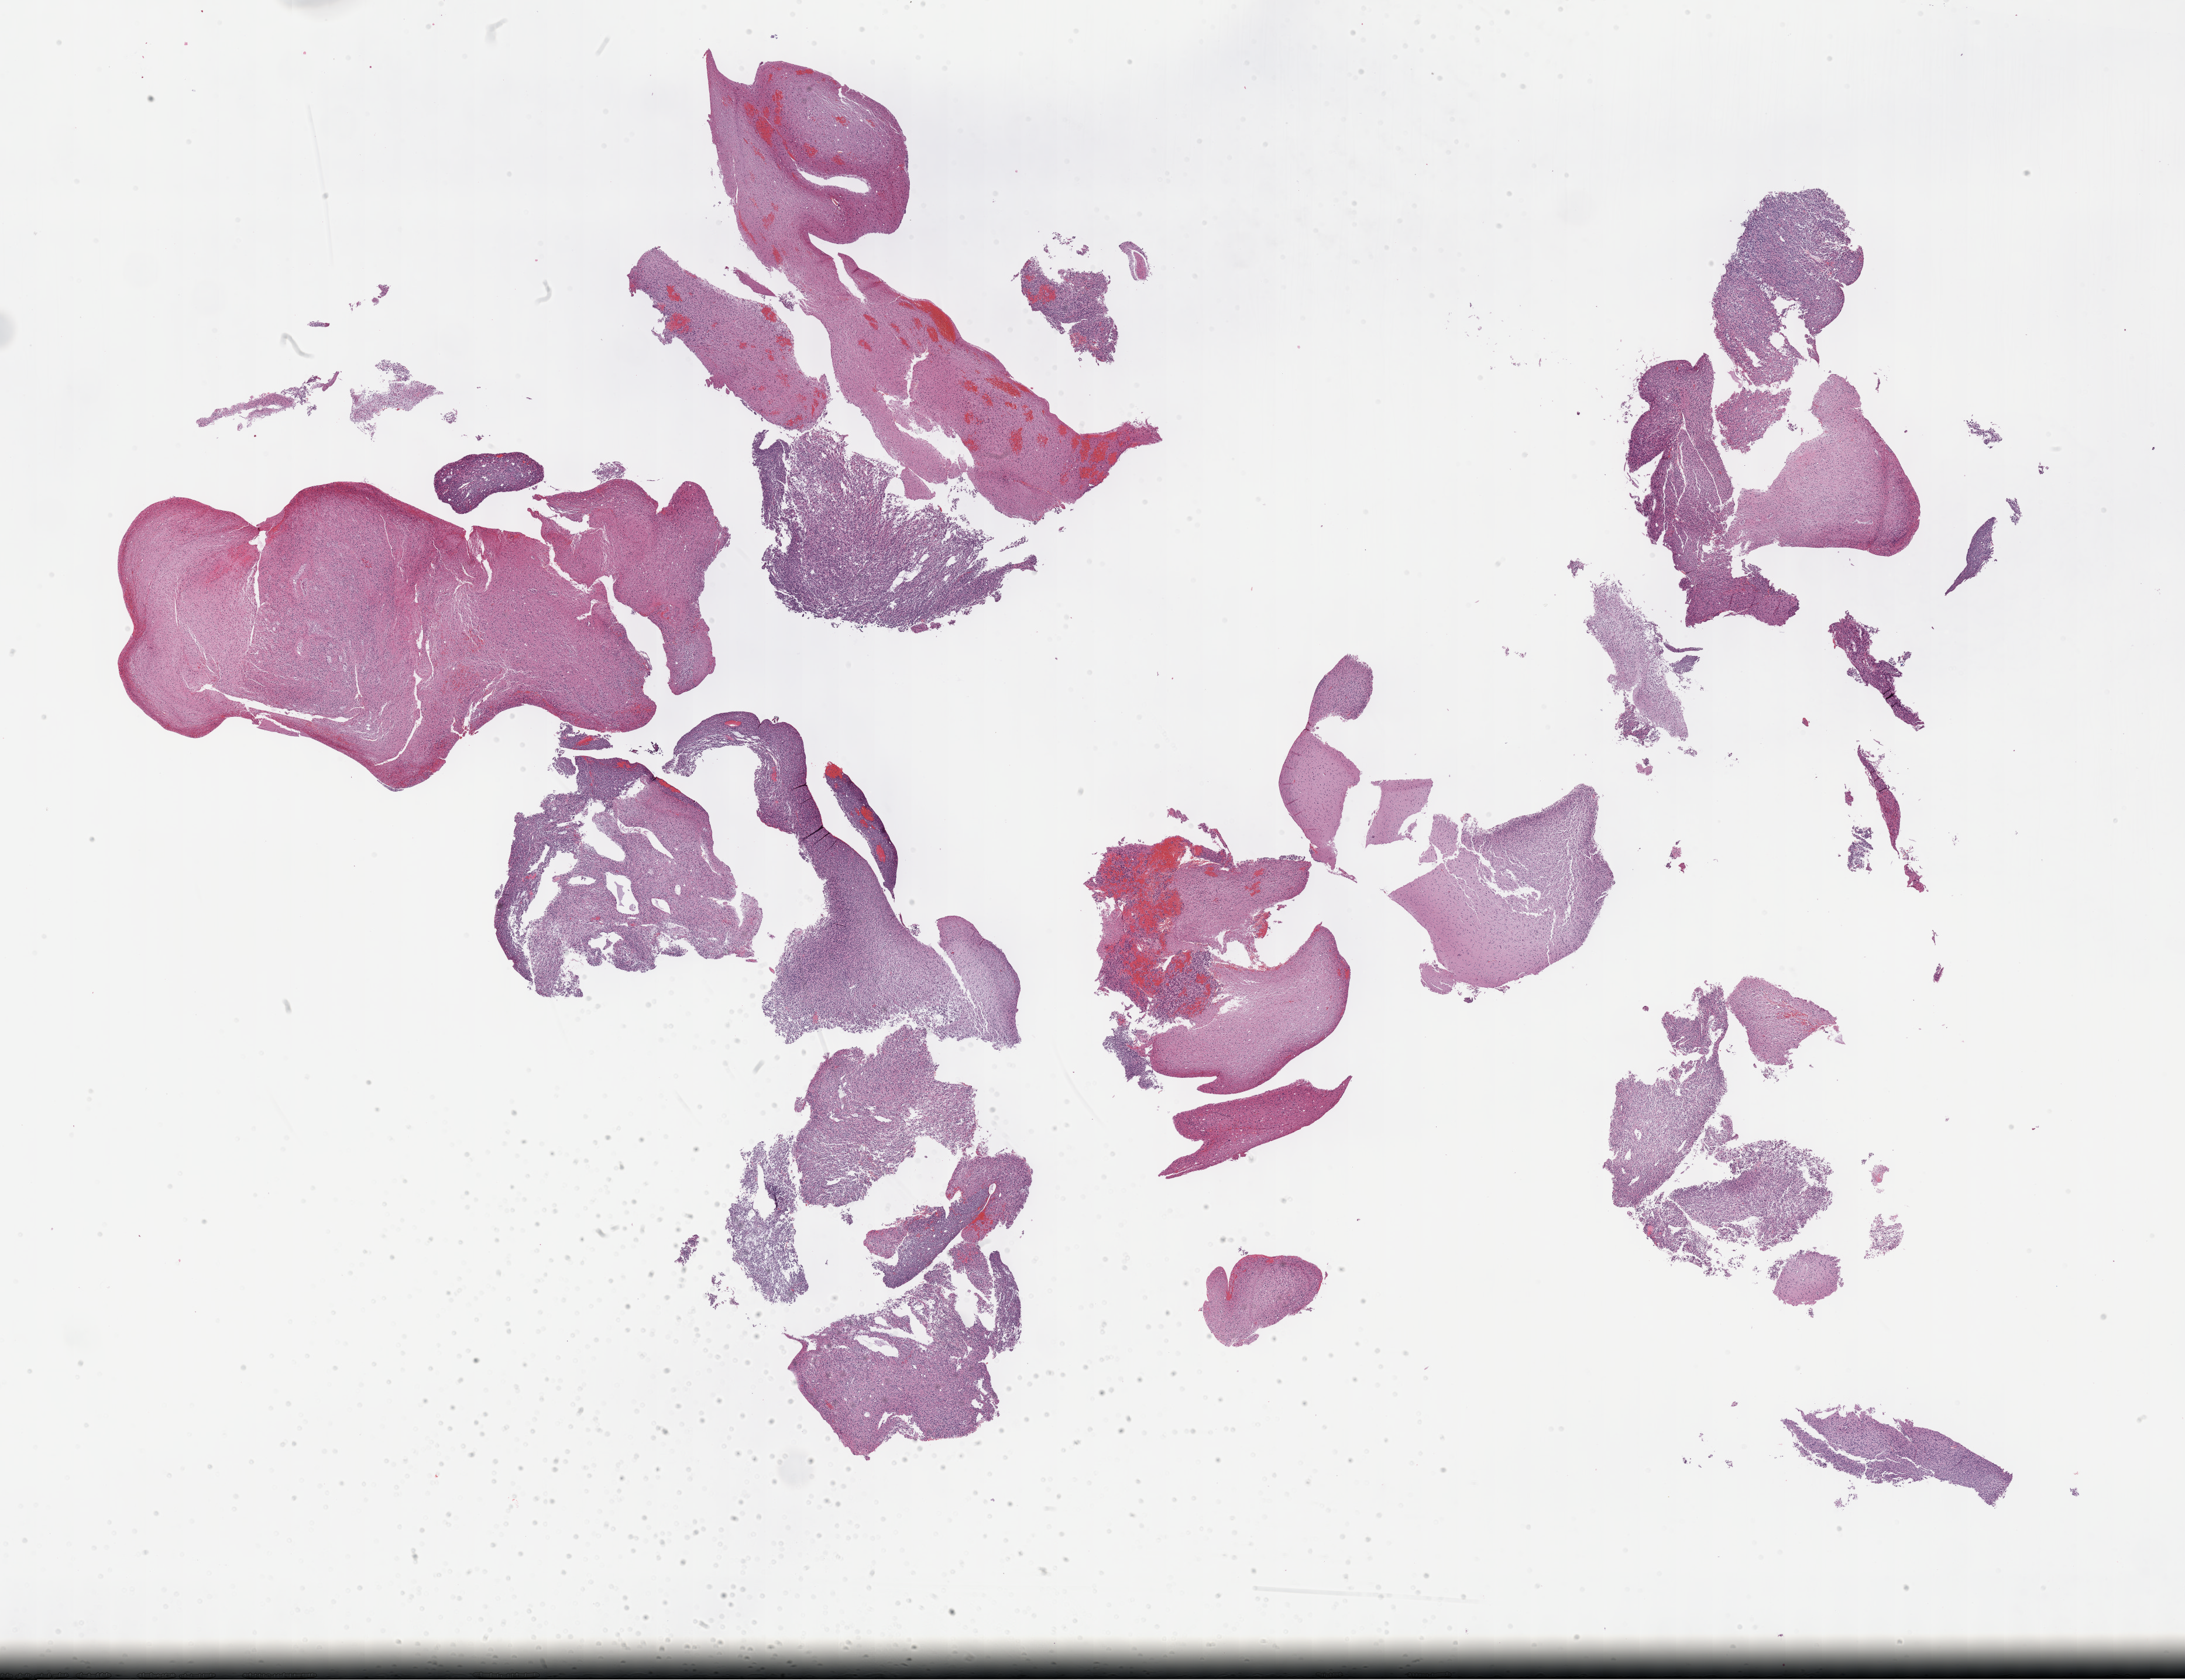
Digitized H&E tissue section (whole slide) — whole scanned area (about 30.2 x 23.2 mm, slide scanned at 40x) shown as a low-resolution overview. Formalin-fixed paraffin-embedded (FFPE) diagnostic section. Primary tumour sample from the brain. Patient: female, age at initial diagnosis 44 years. Histologic grade: G3 (poorly differentiated).
Diagnosis: Astrocytoma, anaplastic (cerebrum). Laterality: left.